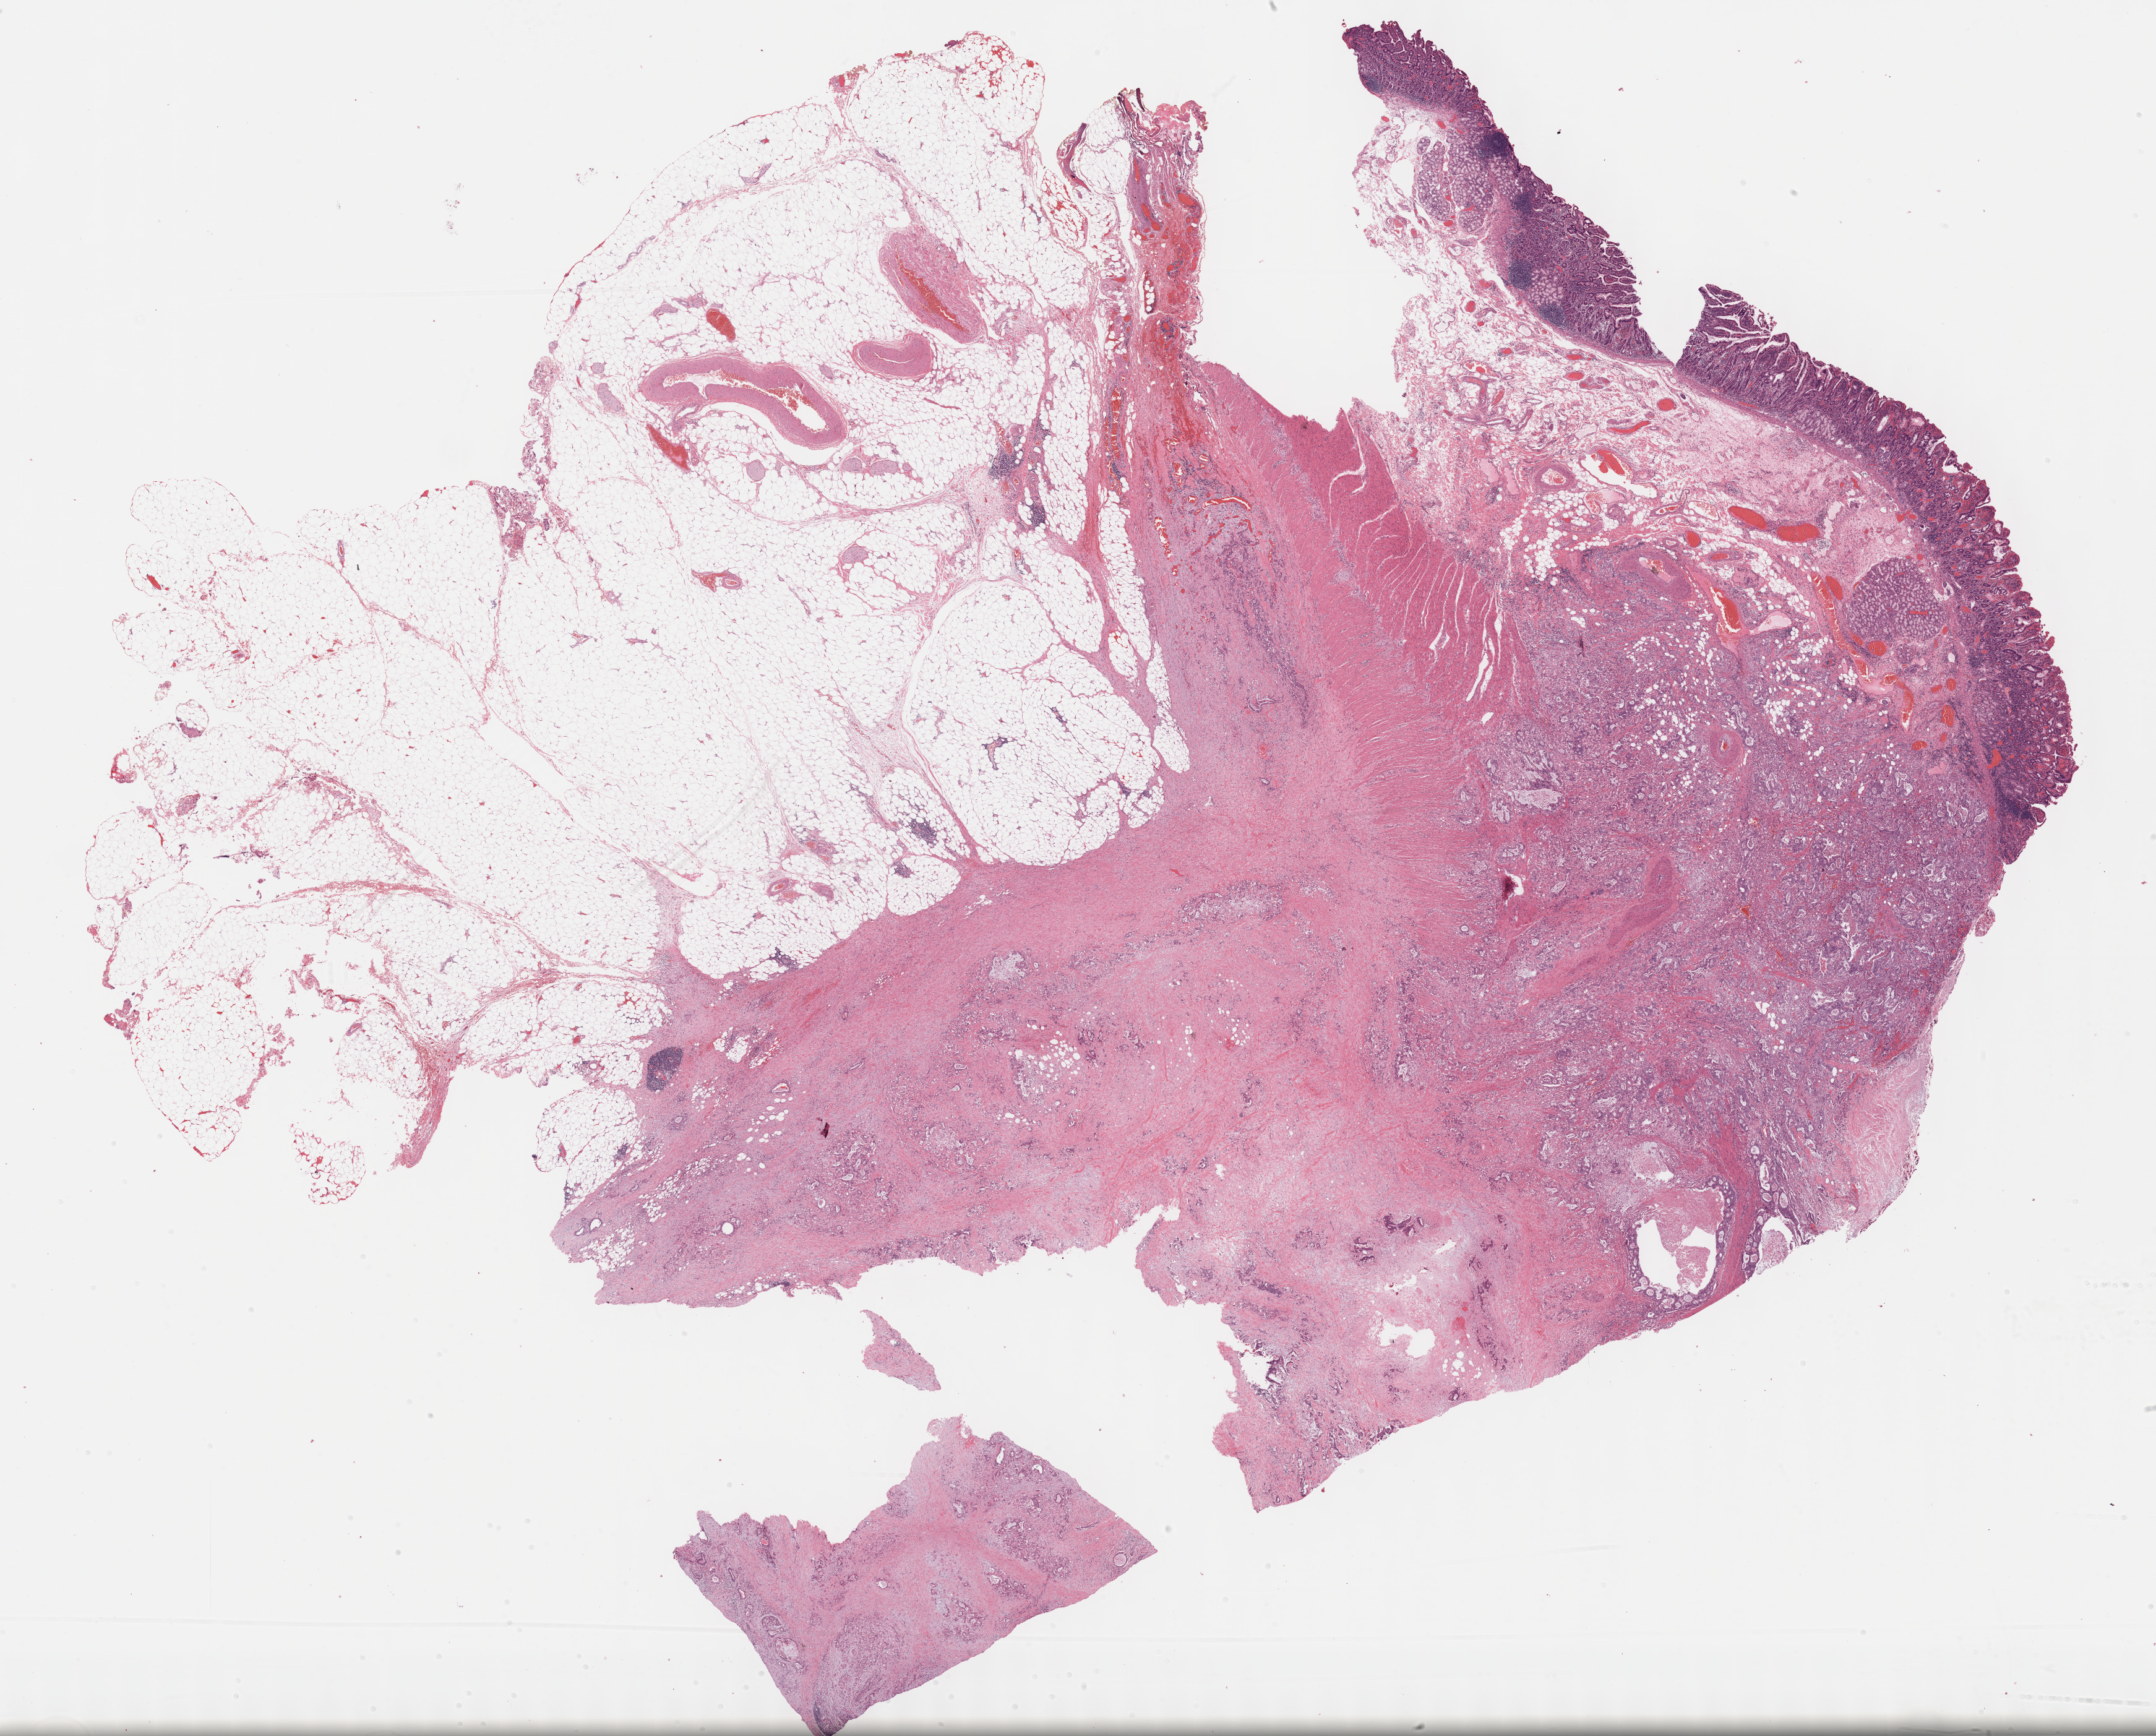
H&E-stained whole-slide image — a low-resolution overview of the entire scanned area, about 28.2 x 22.7 mm, formalin-fixed paraffin-embedded (FFPE) diagnostic section, pancreas, primary tumour sample. Male, age 41 years at initial diagnosis. Histologic grade: G2 (moderately differentiated).
• AJCC pathologic stage: IIB
• pathologic diagnosis: Infiltrating duct carcinoma, NOS (head of pancreas)
• TNM: T3 N1 M0